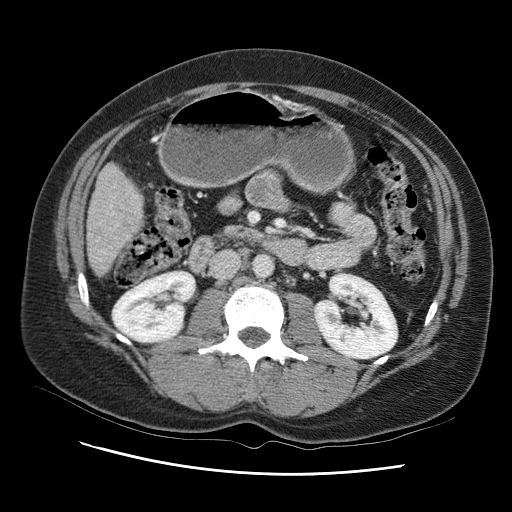
Contrast-enhanced abdominal CT (liver protocol), one axial slice. Position 27 of 95 along the scan axis. Reconstruction kernel STANDARD. 120 kVp. One of 2 acquisitions stored at this slice position. Soft-tissue window (W 400 / L 40 HU). 2.5 mm slice thickness. 512 × 512 image matrix, field of view 360 × 360 mm. Case-level facts recorded for this patient, not image findings: diagnosis: hepatocellular carcinoma (patient treated with transarterial chemoembolisation; whether this scan precedes or follows treatment is not stated here); TNM stage (as recorded): Stage-I; Child-Pugh class: B; tumour differentiation: moderately differentiated; tumour nodularity: uninodular.
Annotated regions visible in this slice (semi-automatic segmentation, software-assisted and operator-edited):
- liver parenchyma outside the tumour (the mass and vessels are separate outlines, so this box may not span the whole liver): bounding box [x1, y1, x2, y2] px = [86, 149, 156, 273]
- liver vessels: [103, 181, 132, 256]